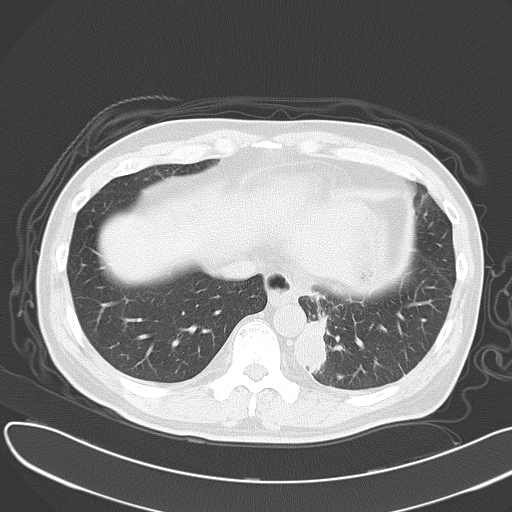
Chest CT, one axial slice; slice 12 of 55 in the series (ordered by position); 120 kVp; lung window (W 1500 / L -600 HU); 5 mm slice thickness; 512 × 512 image matrix, field of view 376 × 376 mm. Patient: male, 55 years. Case-level facts recorded for this patient, not image findings: clinical TNM (as recorded): T2 N3 M0; histopathological grade: G3.
Structures marked on this image (bounding box drawn by a radiologist):
- lung tumour (recorded histology: small cell carcinoma): bounding box <295,310,334,380> (left, top, right, bottom; pixels)